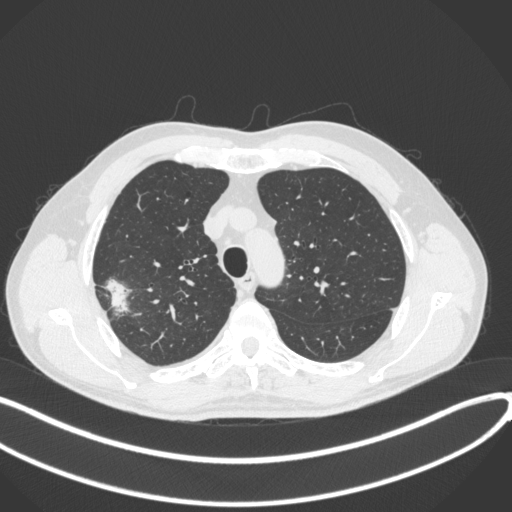
Chest CT, one axial slice; slice 320 of 381 in the series (ordered by position); reconstruction kernel B31f; 120 kVp; lung window (W 1500 / L -600 HU); 512 × 512 image matrix. Male patient, age 62 years. Case-level facts recorded for this patient, not image findings: clinical TNM (as recorded): T1c N0 M0.
Structures marked on this image (bounding box drawn by a radiologist):
- lung tumour (recorded histology: adenocarcinoma): bounding box <104,275,133,320> (left, top, right, bottom; pixels)